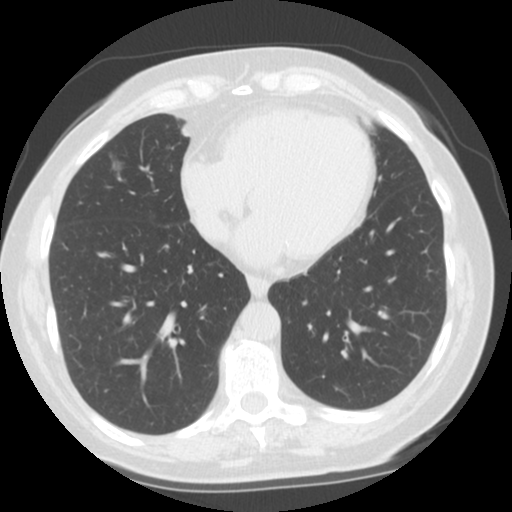
Low-dose screening chest CT, axial slice; baseline annual screen; lung window (W 1500 / L -600 HU); 2.5 mm slice thickness. Female participant, aged 71 years at enrolment. Current smoker at enrolment.
Expert-annotated lung lesion, bounding box [x1, y1, x2, y2] px = [82, 140, 142, 193]. The screening reader recorded 2 non-calcified nodules or masses ≥4 mm on this exam (right middle lobe, left upper lobe); which of them this box marks is not recorded. Official screen result: positive, change unspecified: nodule(s) >= 4 mm or enlarging nodule(s), mass(es), or other non-specific abnormalities suspicious for lung cancer. Lung cancer was diagnosed 491 days after this screen (after the second annual screen): adenocarcinoma, NOS, right middle lobe, moderately differentiated (G2), stage IA (AJCC 6th edition), 12 mm at pathology.